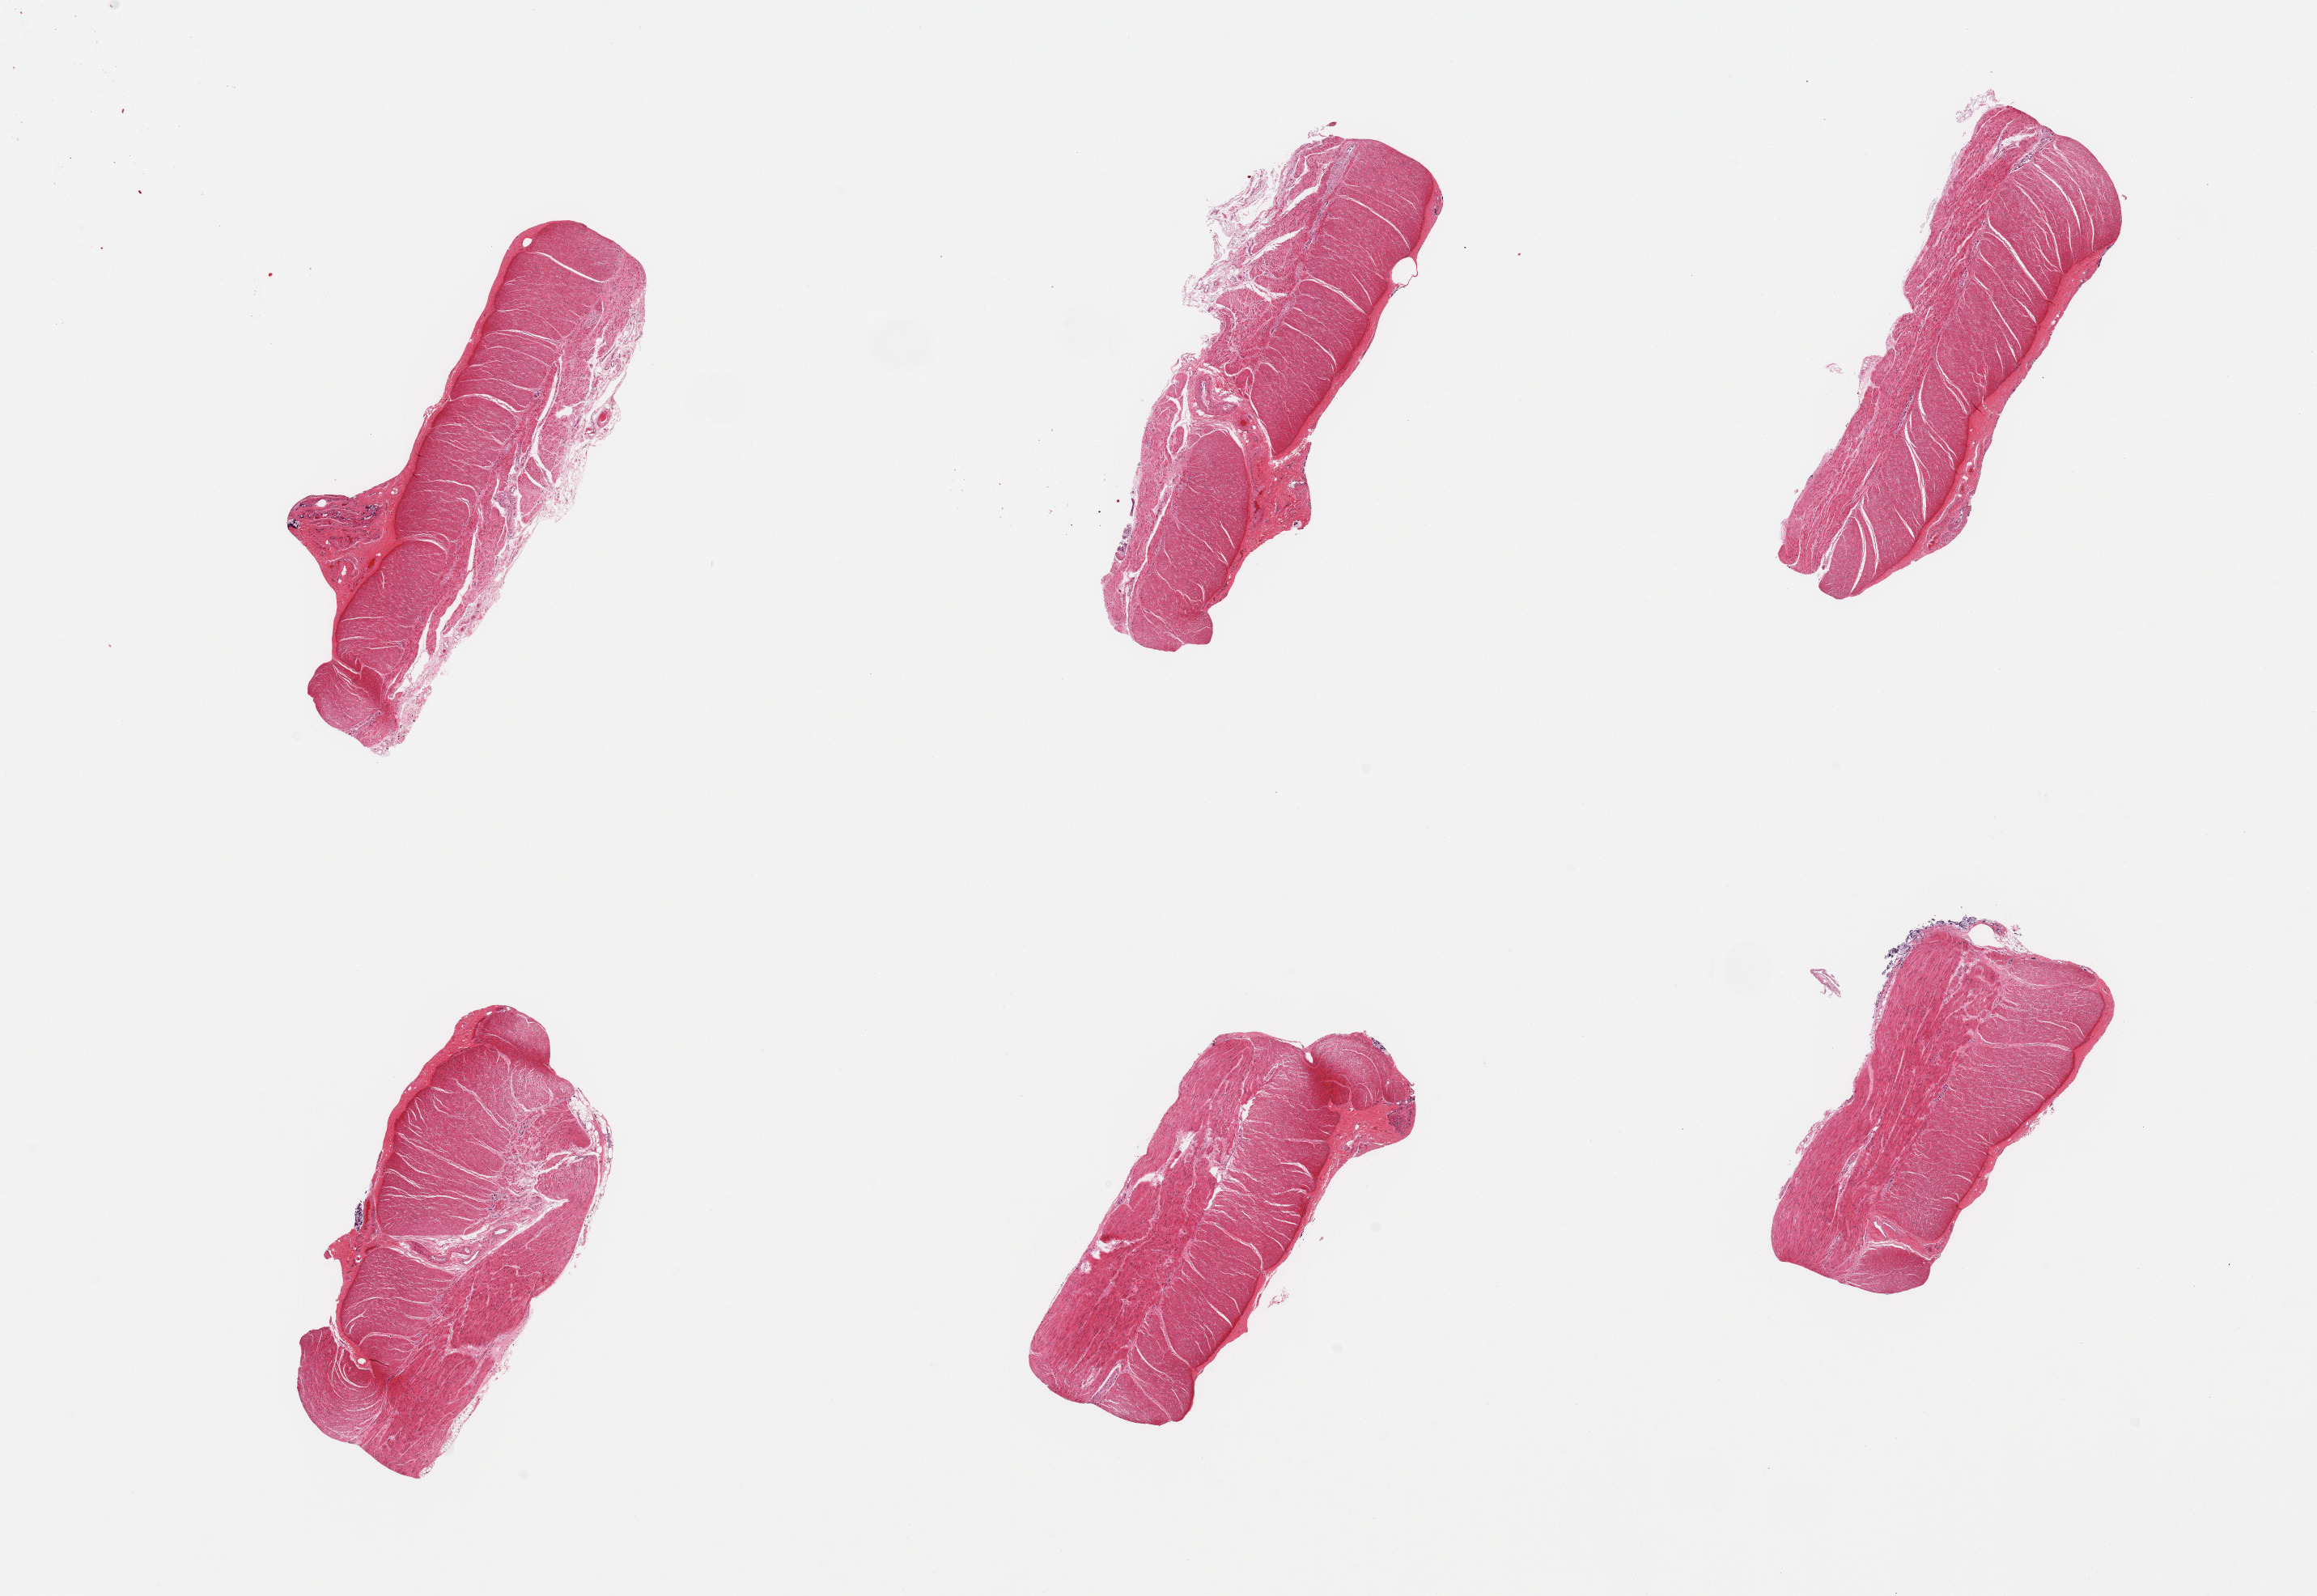
Digitized H&E-stained section, brightfield, whole scanned area (about 22.6 x 15.6 mm, acquisition: 20x scan) shown as a low-resolution overview. PAXgene-fixed, paraffin-embedded tissue. Target tissue: sigmoid colon. Tissue donor sample.
Reviewer comment on this tissue sample: 6 pieces; focal remnants of submucosa, but well dissected intact muscularis.